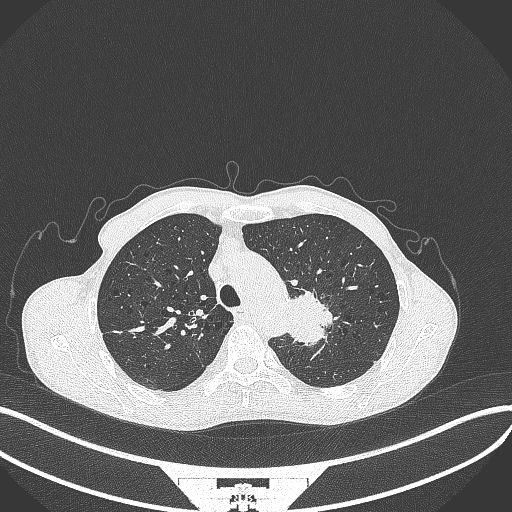
Chest CT, one axial slice. 120 kVp. Lung window (W 1500 / L -600 HU). 512 × 512 image matrix, field of view 400 × 400 mm. Male patient, age 65 years. From the clinical record (not read from this slice): clinical TNM (as recorded): T2b N0 M0; histopathological grade: G2.
Annotated regions visible in this slice (bounding box drawn by a radiologist):
- lung tumour (recorded histology: adenocarcinoma): bounding box <288,287,336,349> (left, top, right, bottom; pixels)